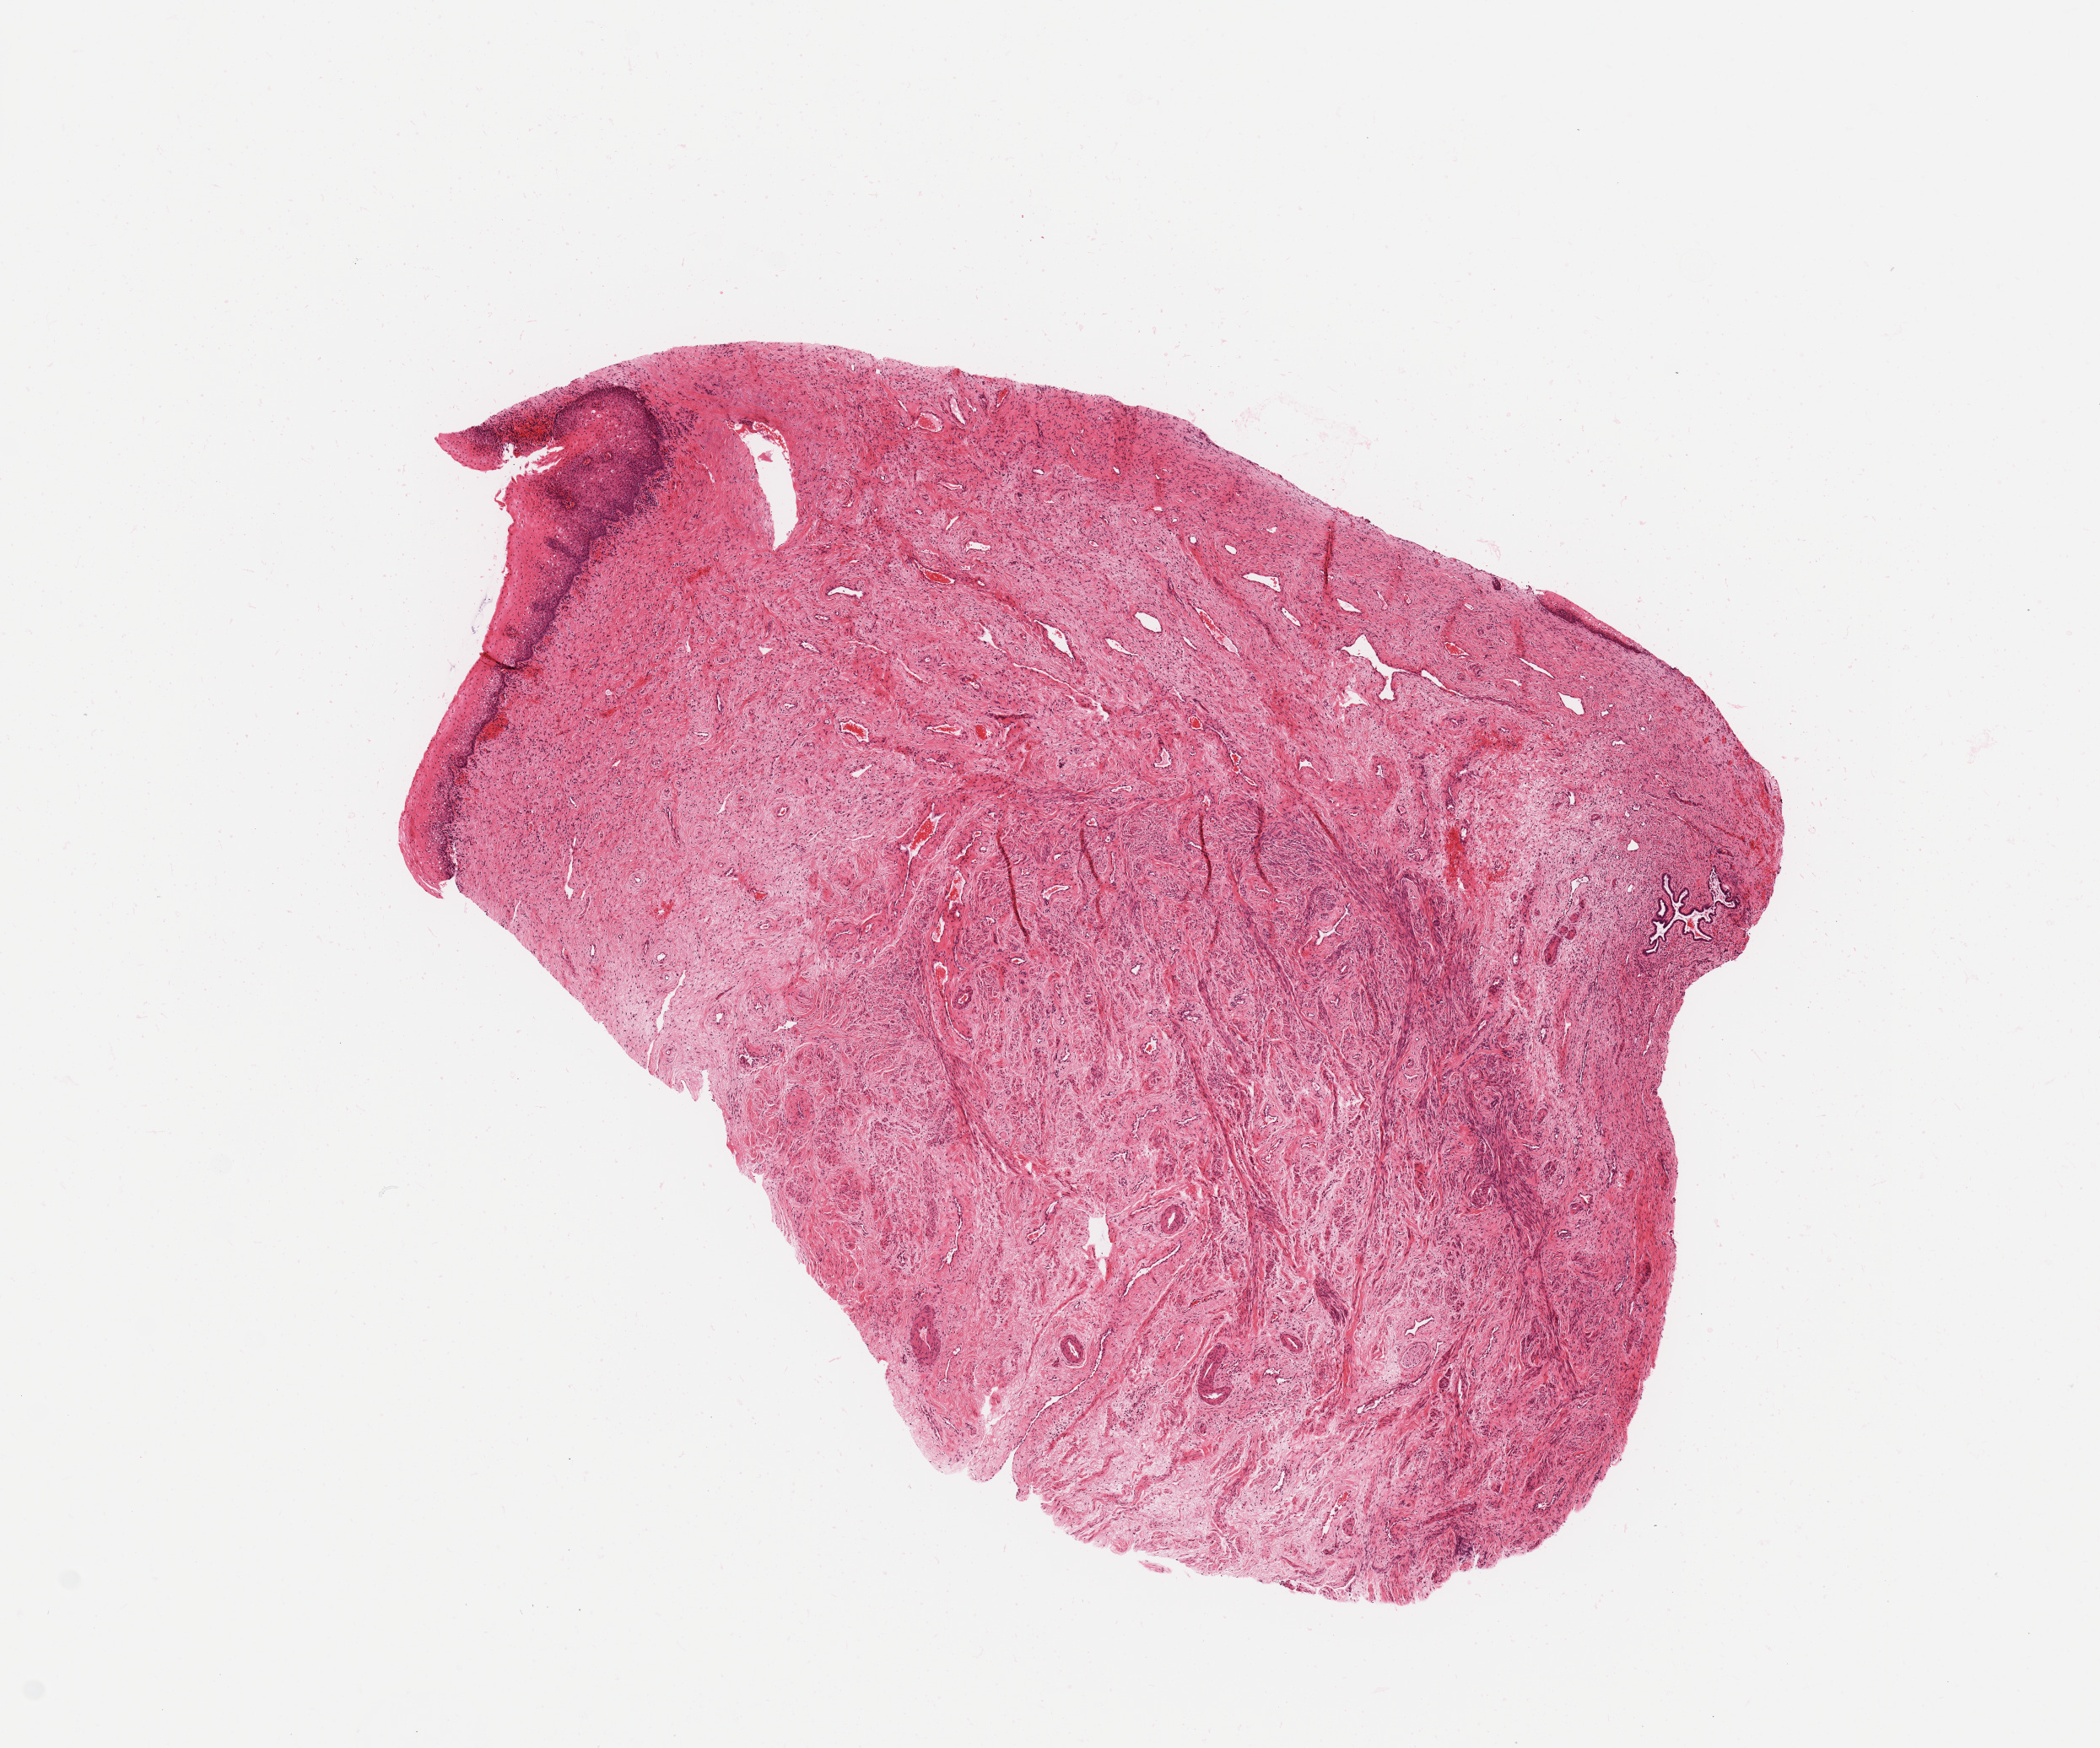
Digitized H&E tissue section (whole slide) — low-resolution overview of the scanned area, about 9.8 x 8.2 mm, uterus, normal (non-tumour) tissue. Patient: female, age 59 years.
This section: normal (non-tumour) tissue from the same patient. Patient diagnosis: Endometrioid adenocarcinoma, NOS.